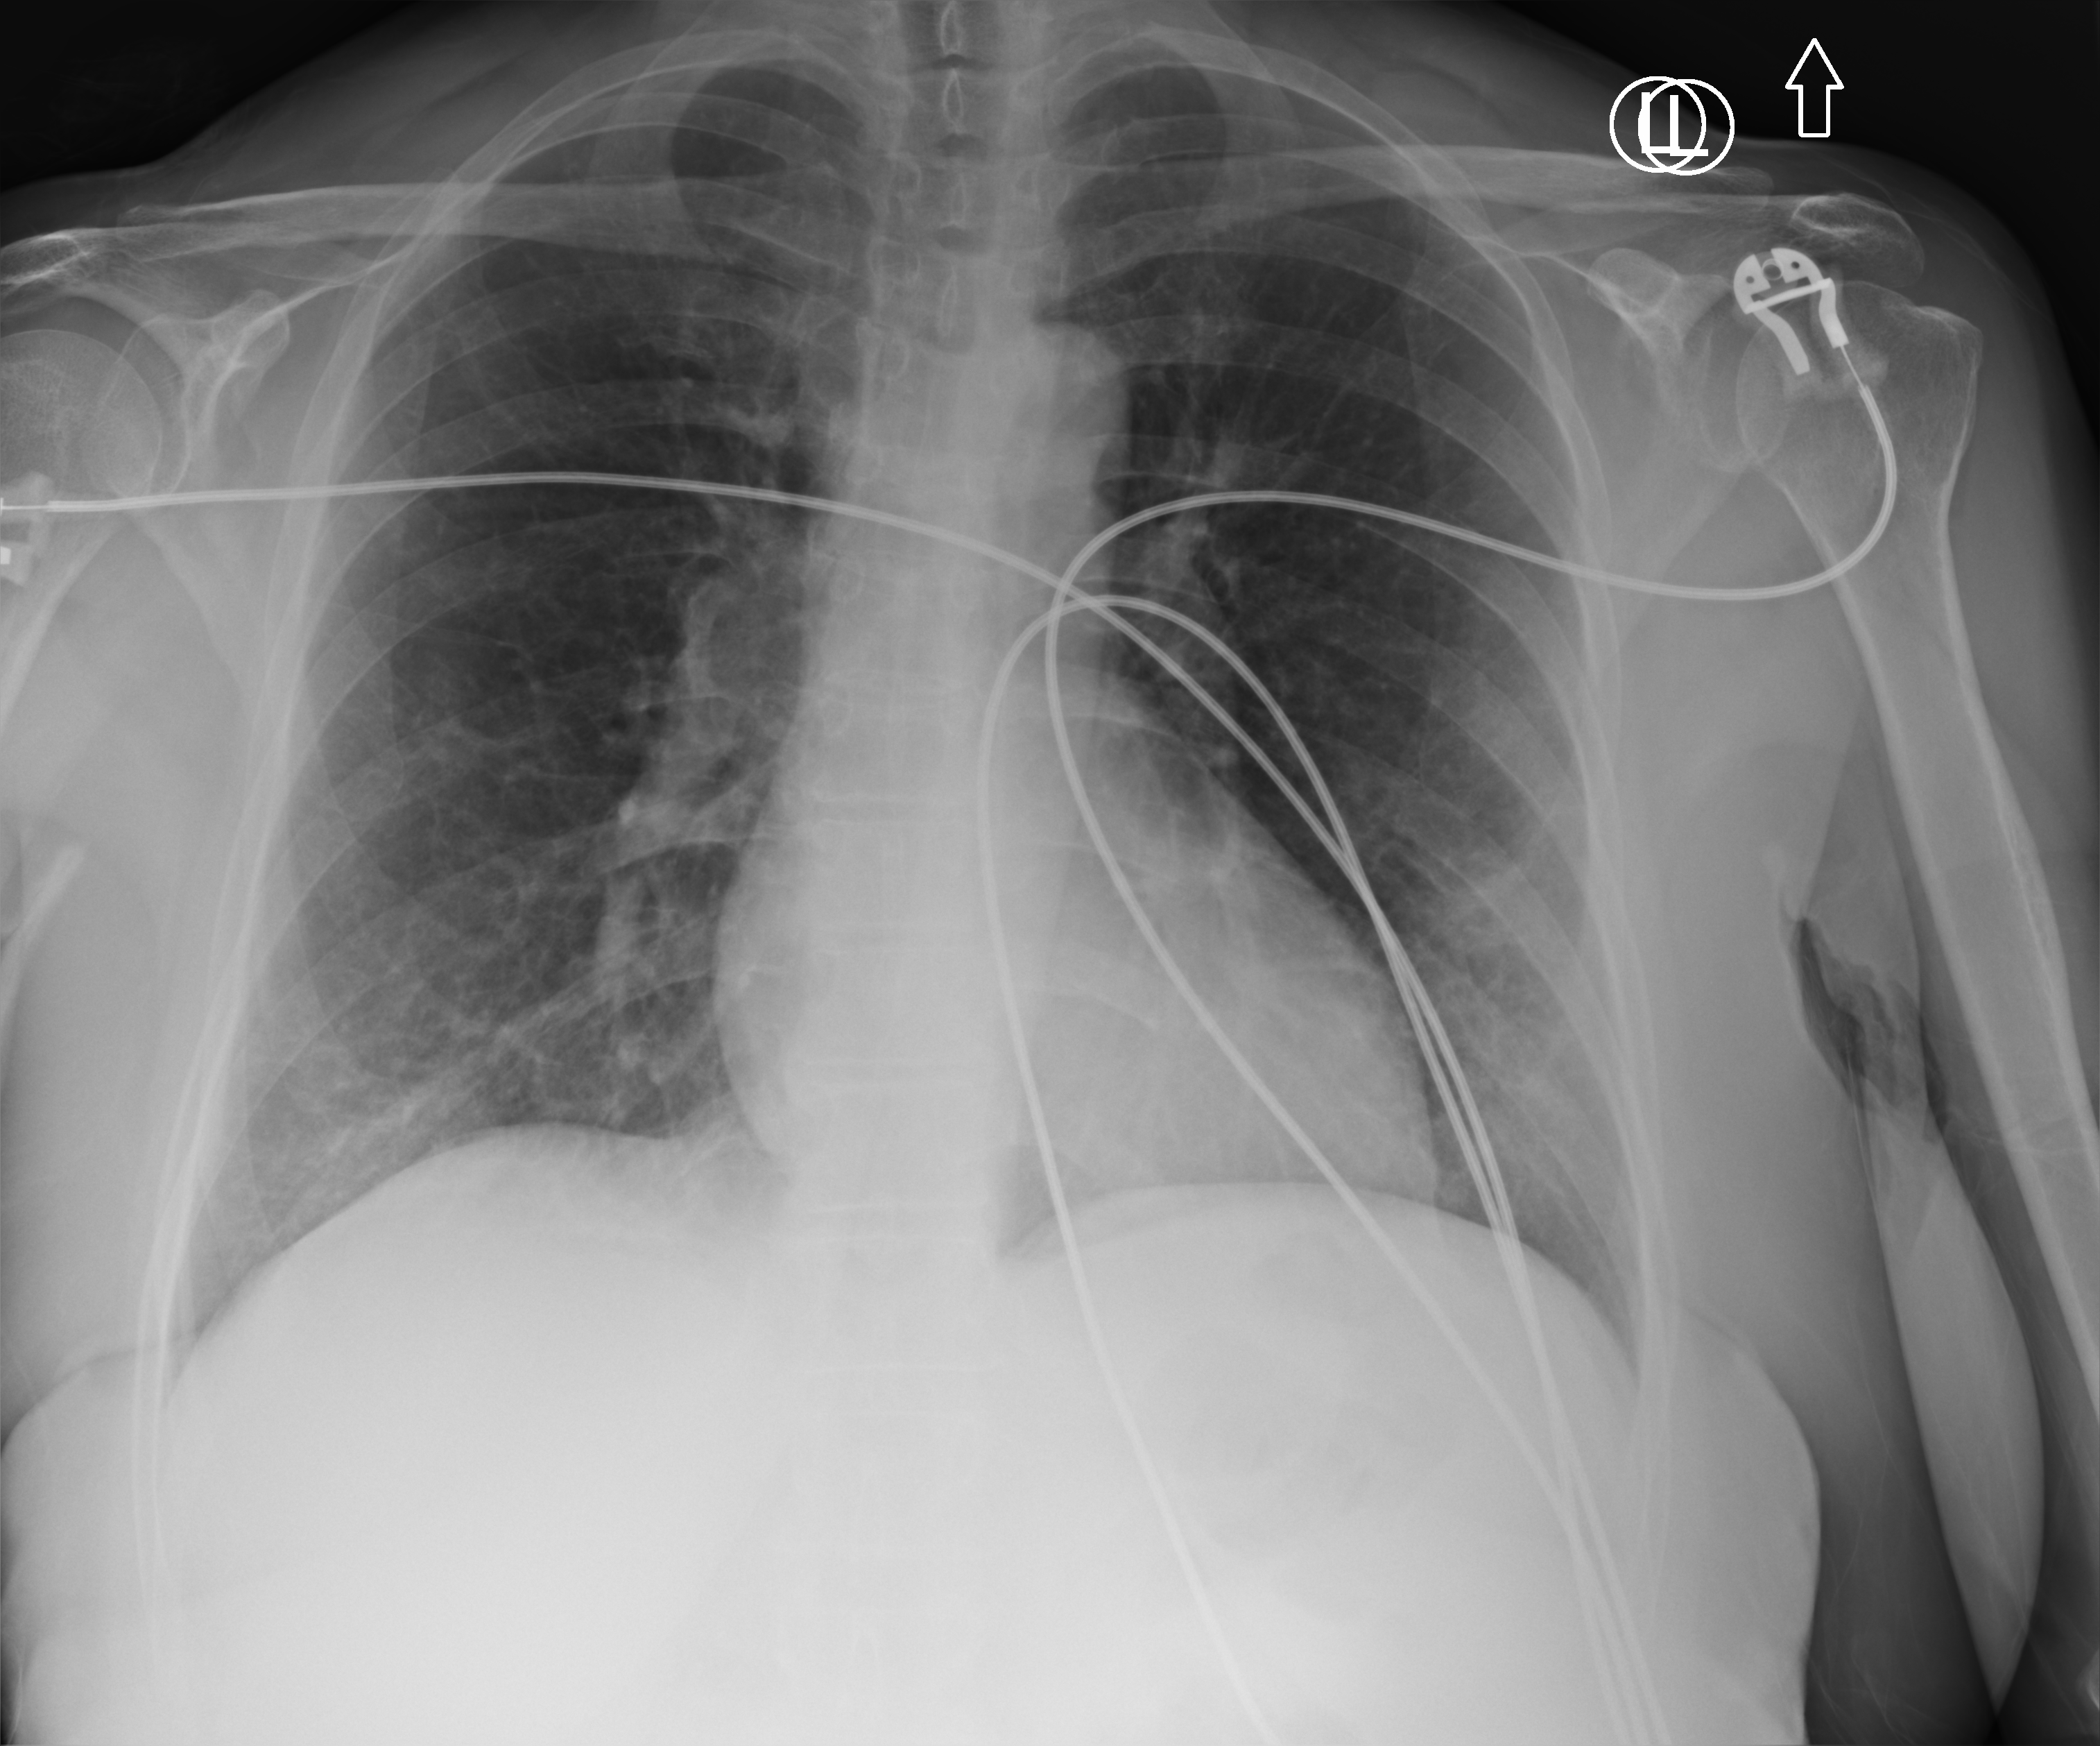
Portable chest radiograph. Female patient hospitalised with COVID-19, age 60–74 years.
From the hospital-stay record, not from the radiograph (when in the stay this image was taken is not recorded): mechanically ventilated during this hospital stay: no; chronic kidney disease (admission record): no.